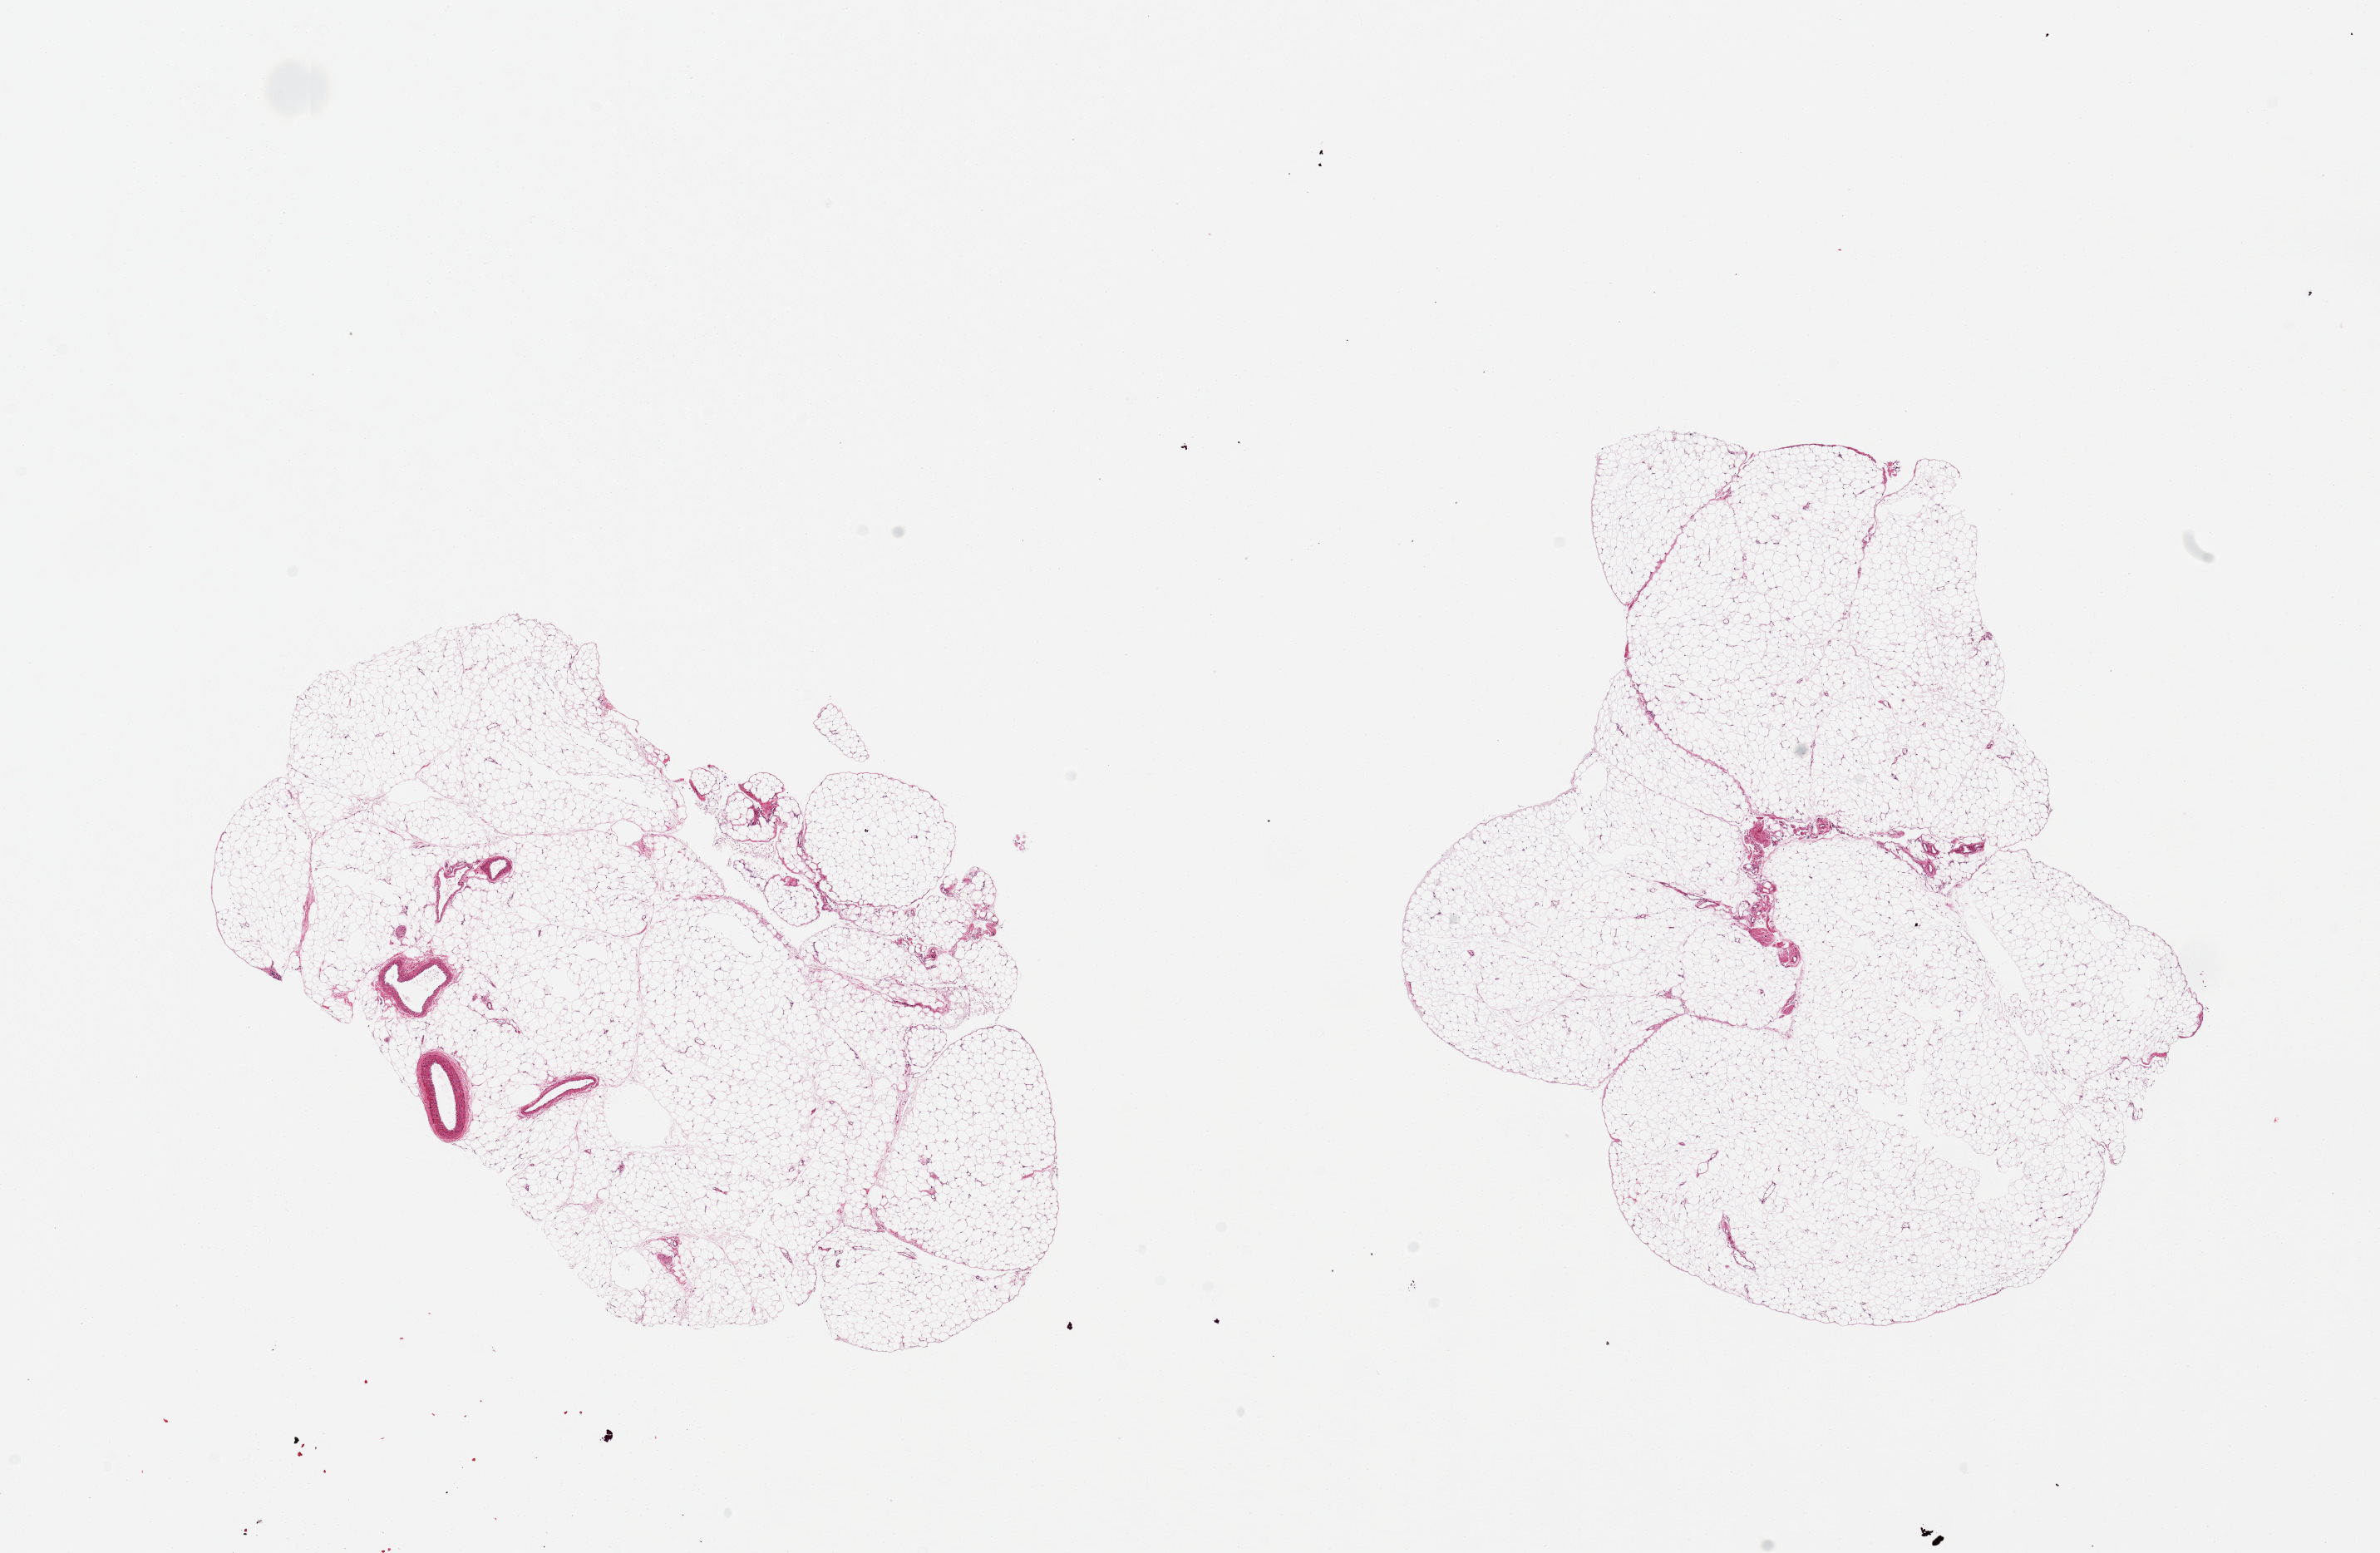
Whole-slide image, haematoxylin and eosin stain — low-resolution overview of the scanned area, about 22.6 x 14.8 mm; PAXgene-fixed paraffin-embedded (PFPE) section; sampled site (target tissue): omentum; tissue donor sample. Donor sex: male.
Review note (as recorded): 2 pieces, 9x6 & 8x7mm.